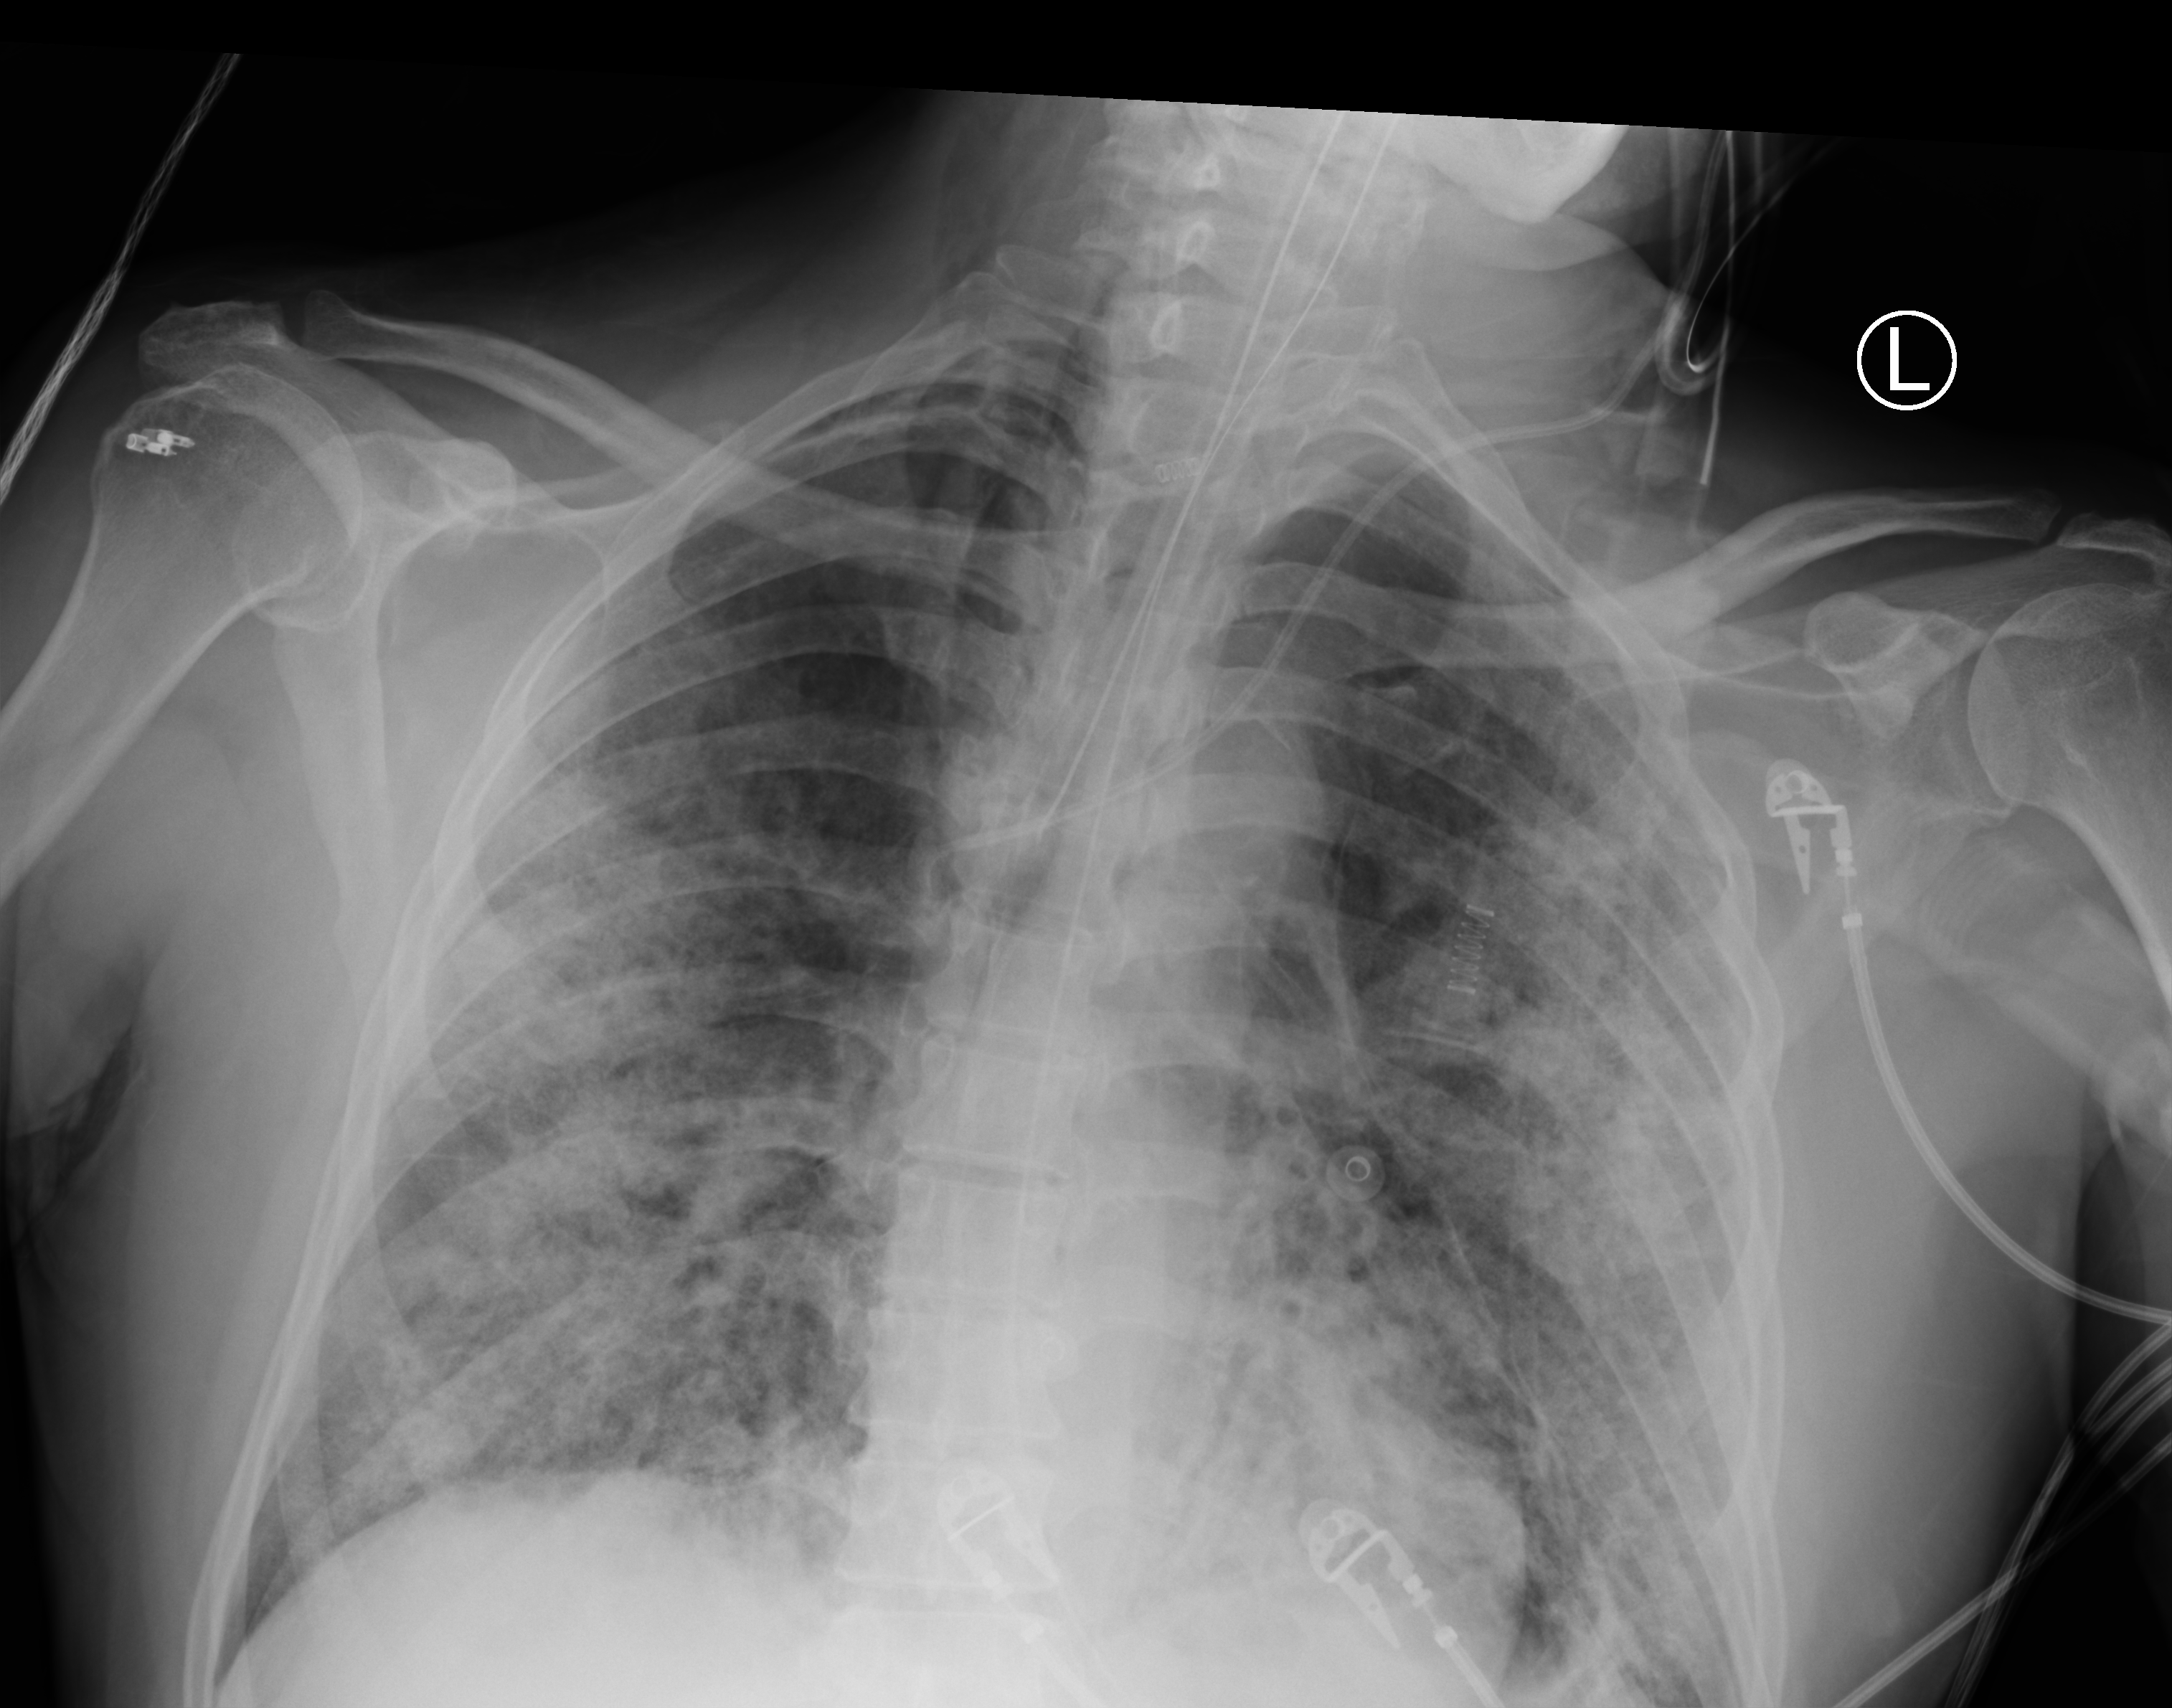
Bedside chest radiograph (computed radiography); anteroposterior (AP) projection. Patient hospitalised with COVID-19; male, aged 60–74 years.
Admission-level facts for this patient (not findings on this image; timing relative to this image not recorded): mechanically ventilated during this hospital stay: yes; smoking status (admission record): never; admitted to intensive care during this hospital stay: yes.